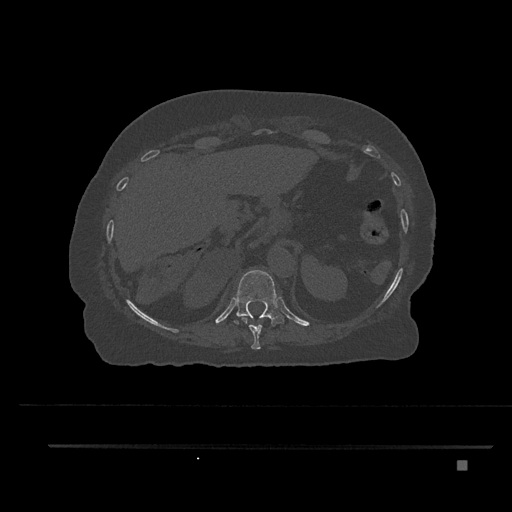
CT including the spine, one axial slice. Position 325 of 797 along the scan axis. Reconstruction kernel Br40s/3. 120 kVp. Bone window (W 1800 / L 400 HU). 512 × 512 image matrix, field of view 437 × 437 mm. Female patient, age 76 years. From the clinical record (not read from this slice): primary cancer: lung; vertebrae with lytic lesions (as recorded): T11, L3.
Outlined on this slice (semi-automatic segmentation, software-assisted and operator-edited):
- T10 vertebra: box from (x=241, y=317) to (x=263, y=350) px
- T11 vertebra: (x=234, y=270)–(x=284, y=326)